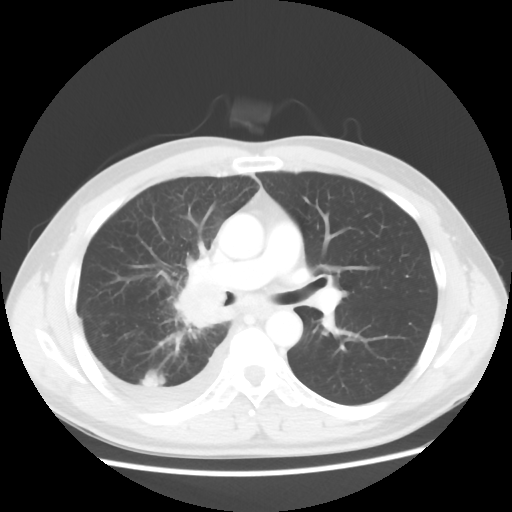
Chest CT, one axial slice. Reconstruction kernel STANDARD. 120 kVp. Lung window (W 1500 / L -600 HU). 5 mm slice thickness. 512 × 512 image matrix, field of view 360 × 360 mm. Male patient, age 46 years. From the clinical record (not read from this slice): clinical TNM (as recorded): T2 N3 M1.
Annotated regions visible in this slice (bounding box drawn by a radiologist):
- lung tumour (recorded histology: adenocarcinoma): bounding box (x1, y1, x2, y2) in pixels: (174, 277, 229, 339)